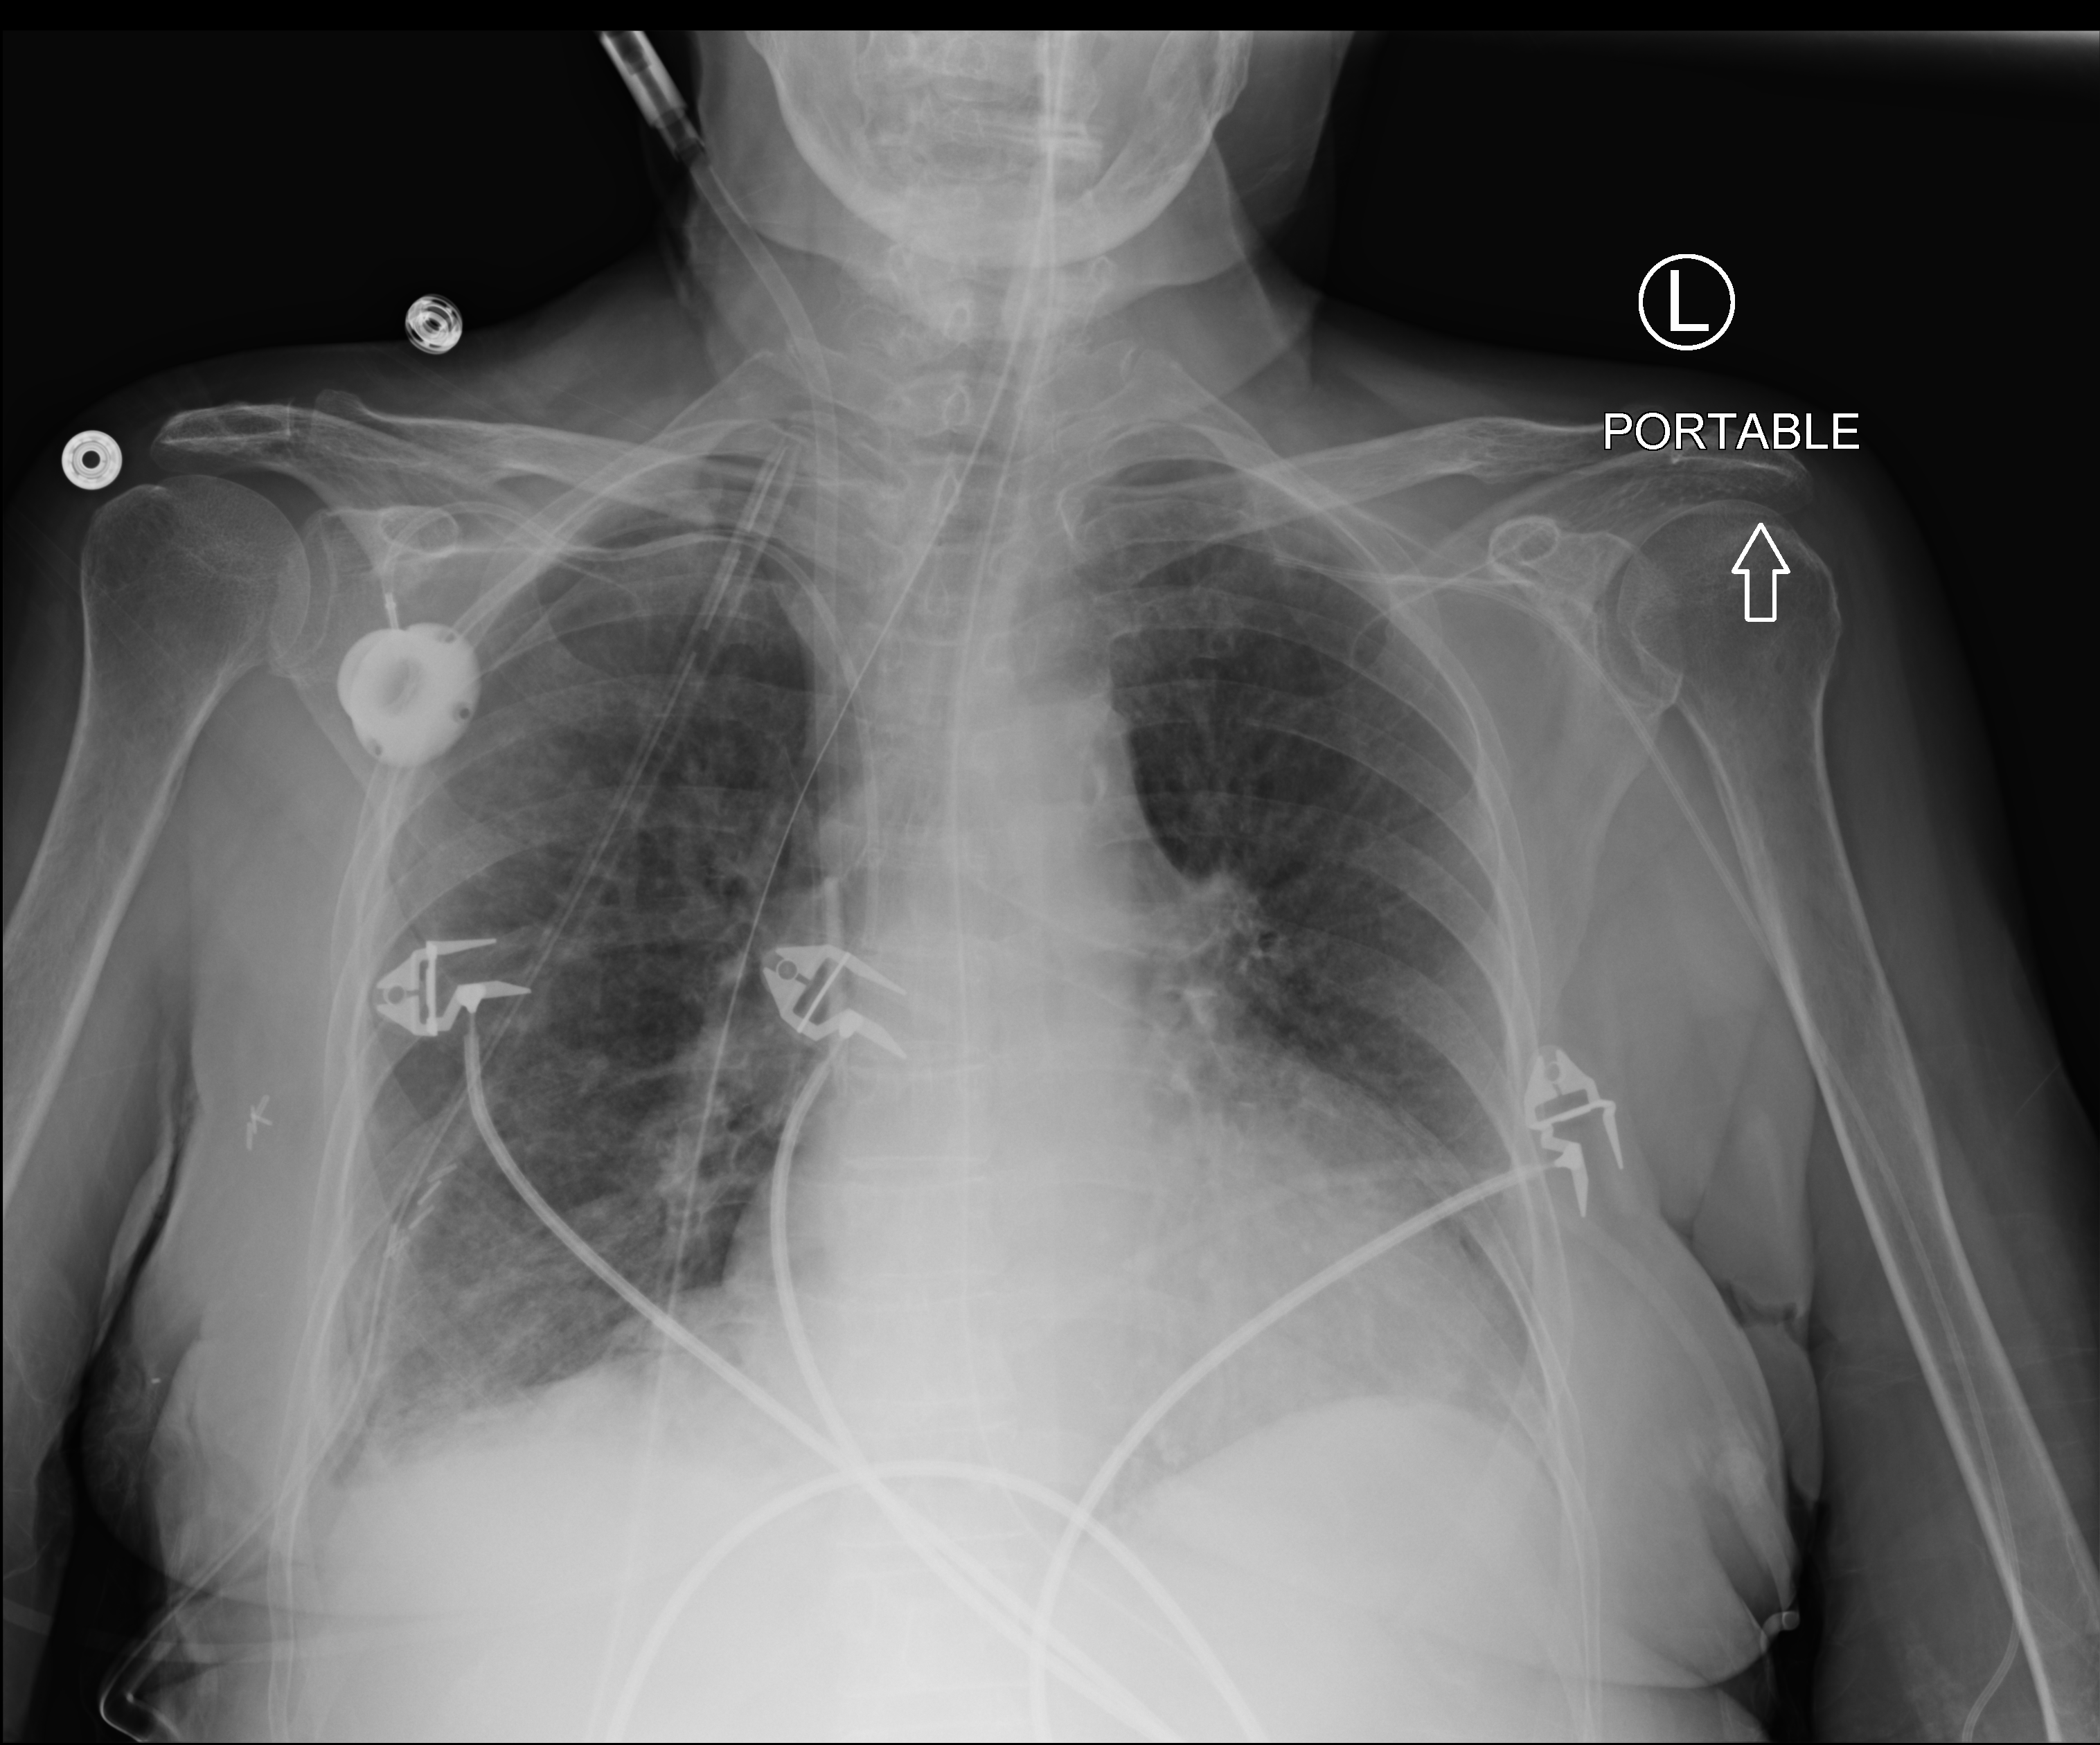
Portable chest radiograph, anteroposterior (AP) projection. Female patient hospitalised with COVID-19, age 60–74 years.
Admission-level facts for this patient (not findings on this image; timing relative to this image not recorded): mechanically ventilated during this hospital stay: yes; admitted to intensive care during this hospital stay: yes.